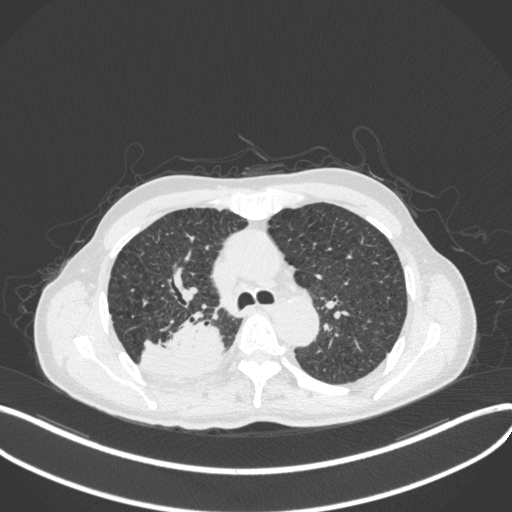
Chest CT, one axial slice; slice 307 of 423 in the series (ordered by position); reconstruction kernel B31f; lung window (W 1500 / L -600 HU); 1 mm slice thickness; 512 × 512 image matrix. Patient: male, 79 years. Case-level facts recorded for this patient, not image findings: clinical TNM (as recorded): T3 N0 M0.
Structures marked on this image (rectangle marked by the reading radiologist):
- lung tumour (recorded histology: adenocarcinoma): bounding box [x1, y1, x2, y2] px = [142, 312, 227, 379]